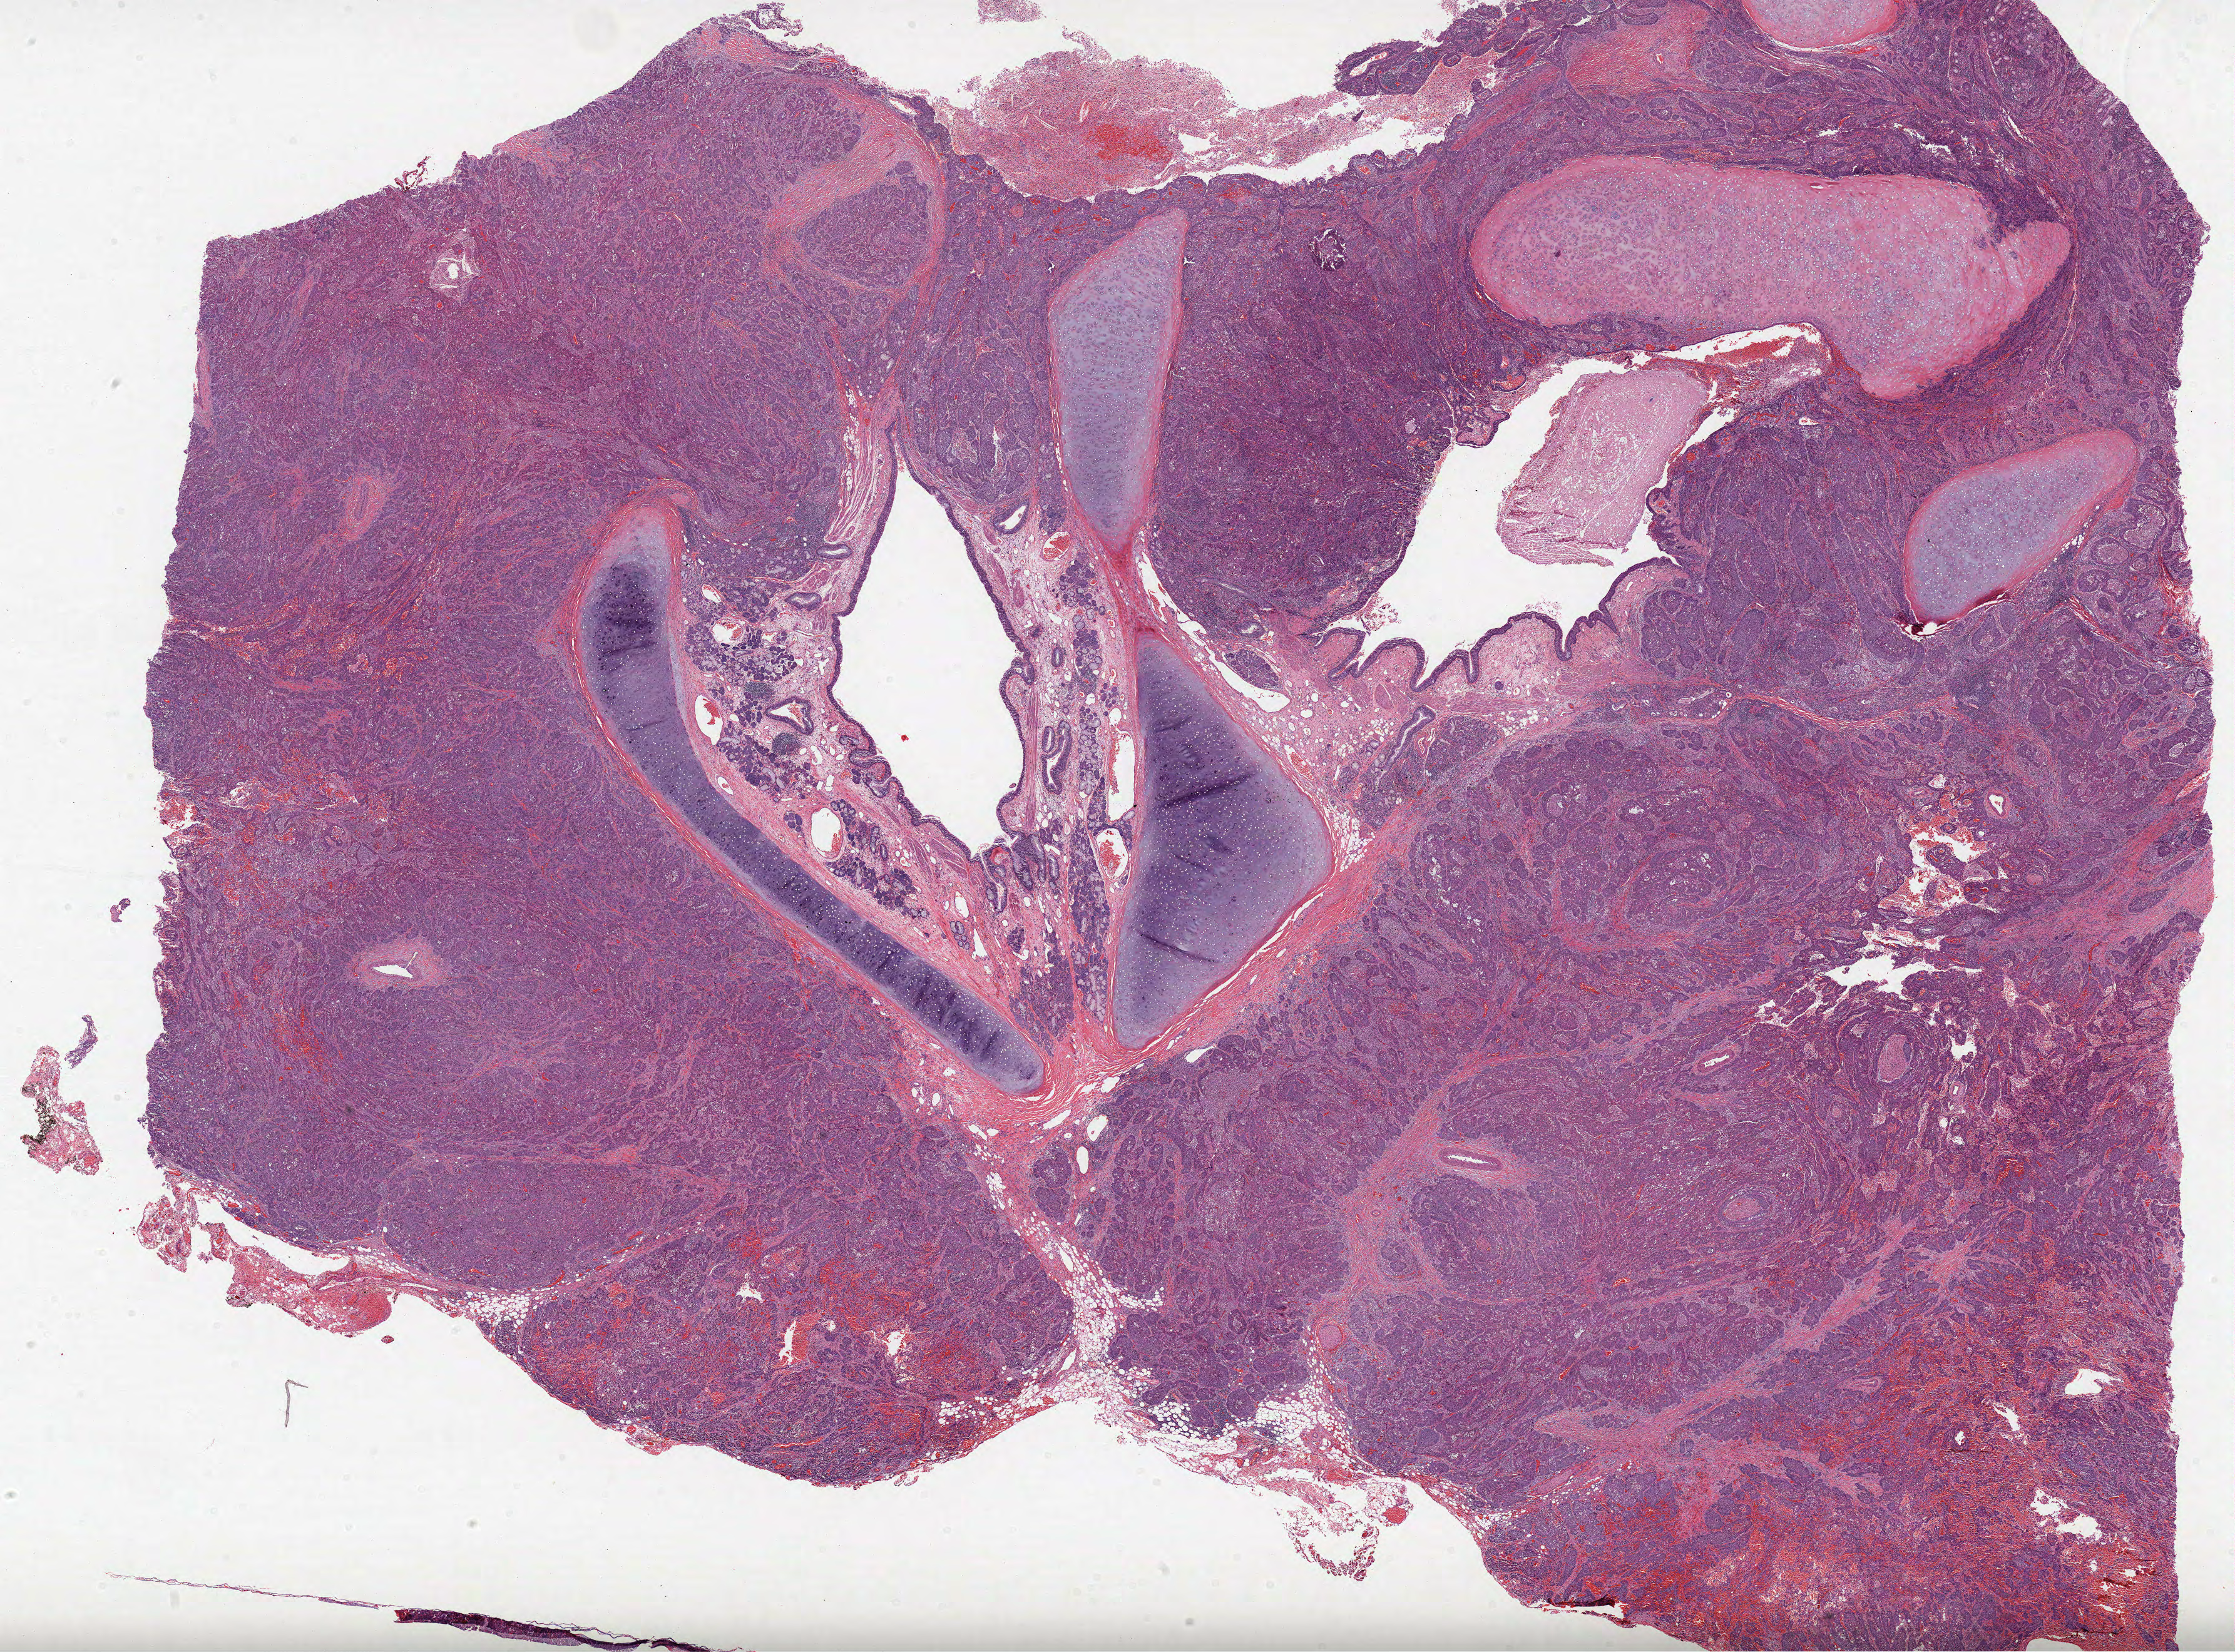
Digitized H&E-stained tissue section (whole slide), whole scanned area (about 28.8 x 21.3 mm) shown as a low-resolution overview; formalin-fixed paraffin-embedded (FFPE) diagnostic section; primary tumour sample from the lung. Male patient; age at initial diagnosis 44 years.
* AJCC pathologic stage: IIA
* diagnosis: Basaloid squamous cell carcinoma
* laterality: right